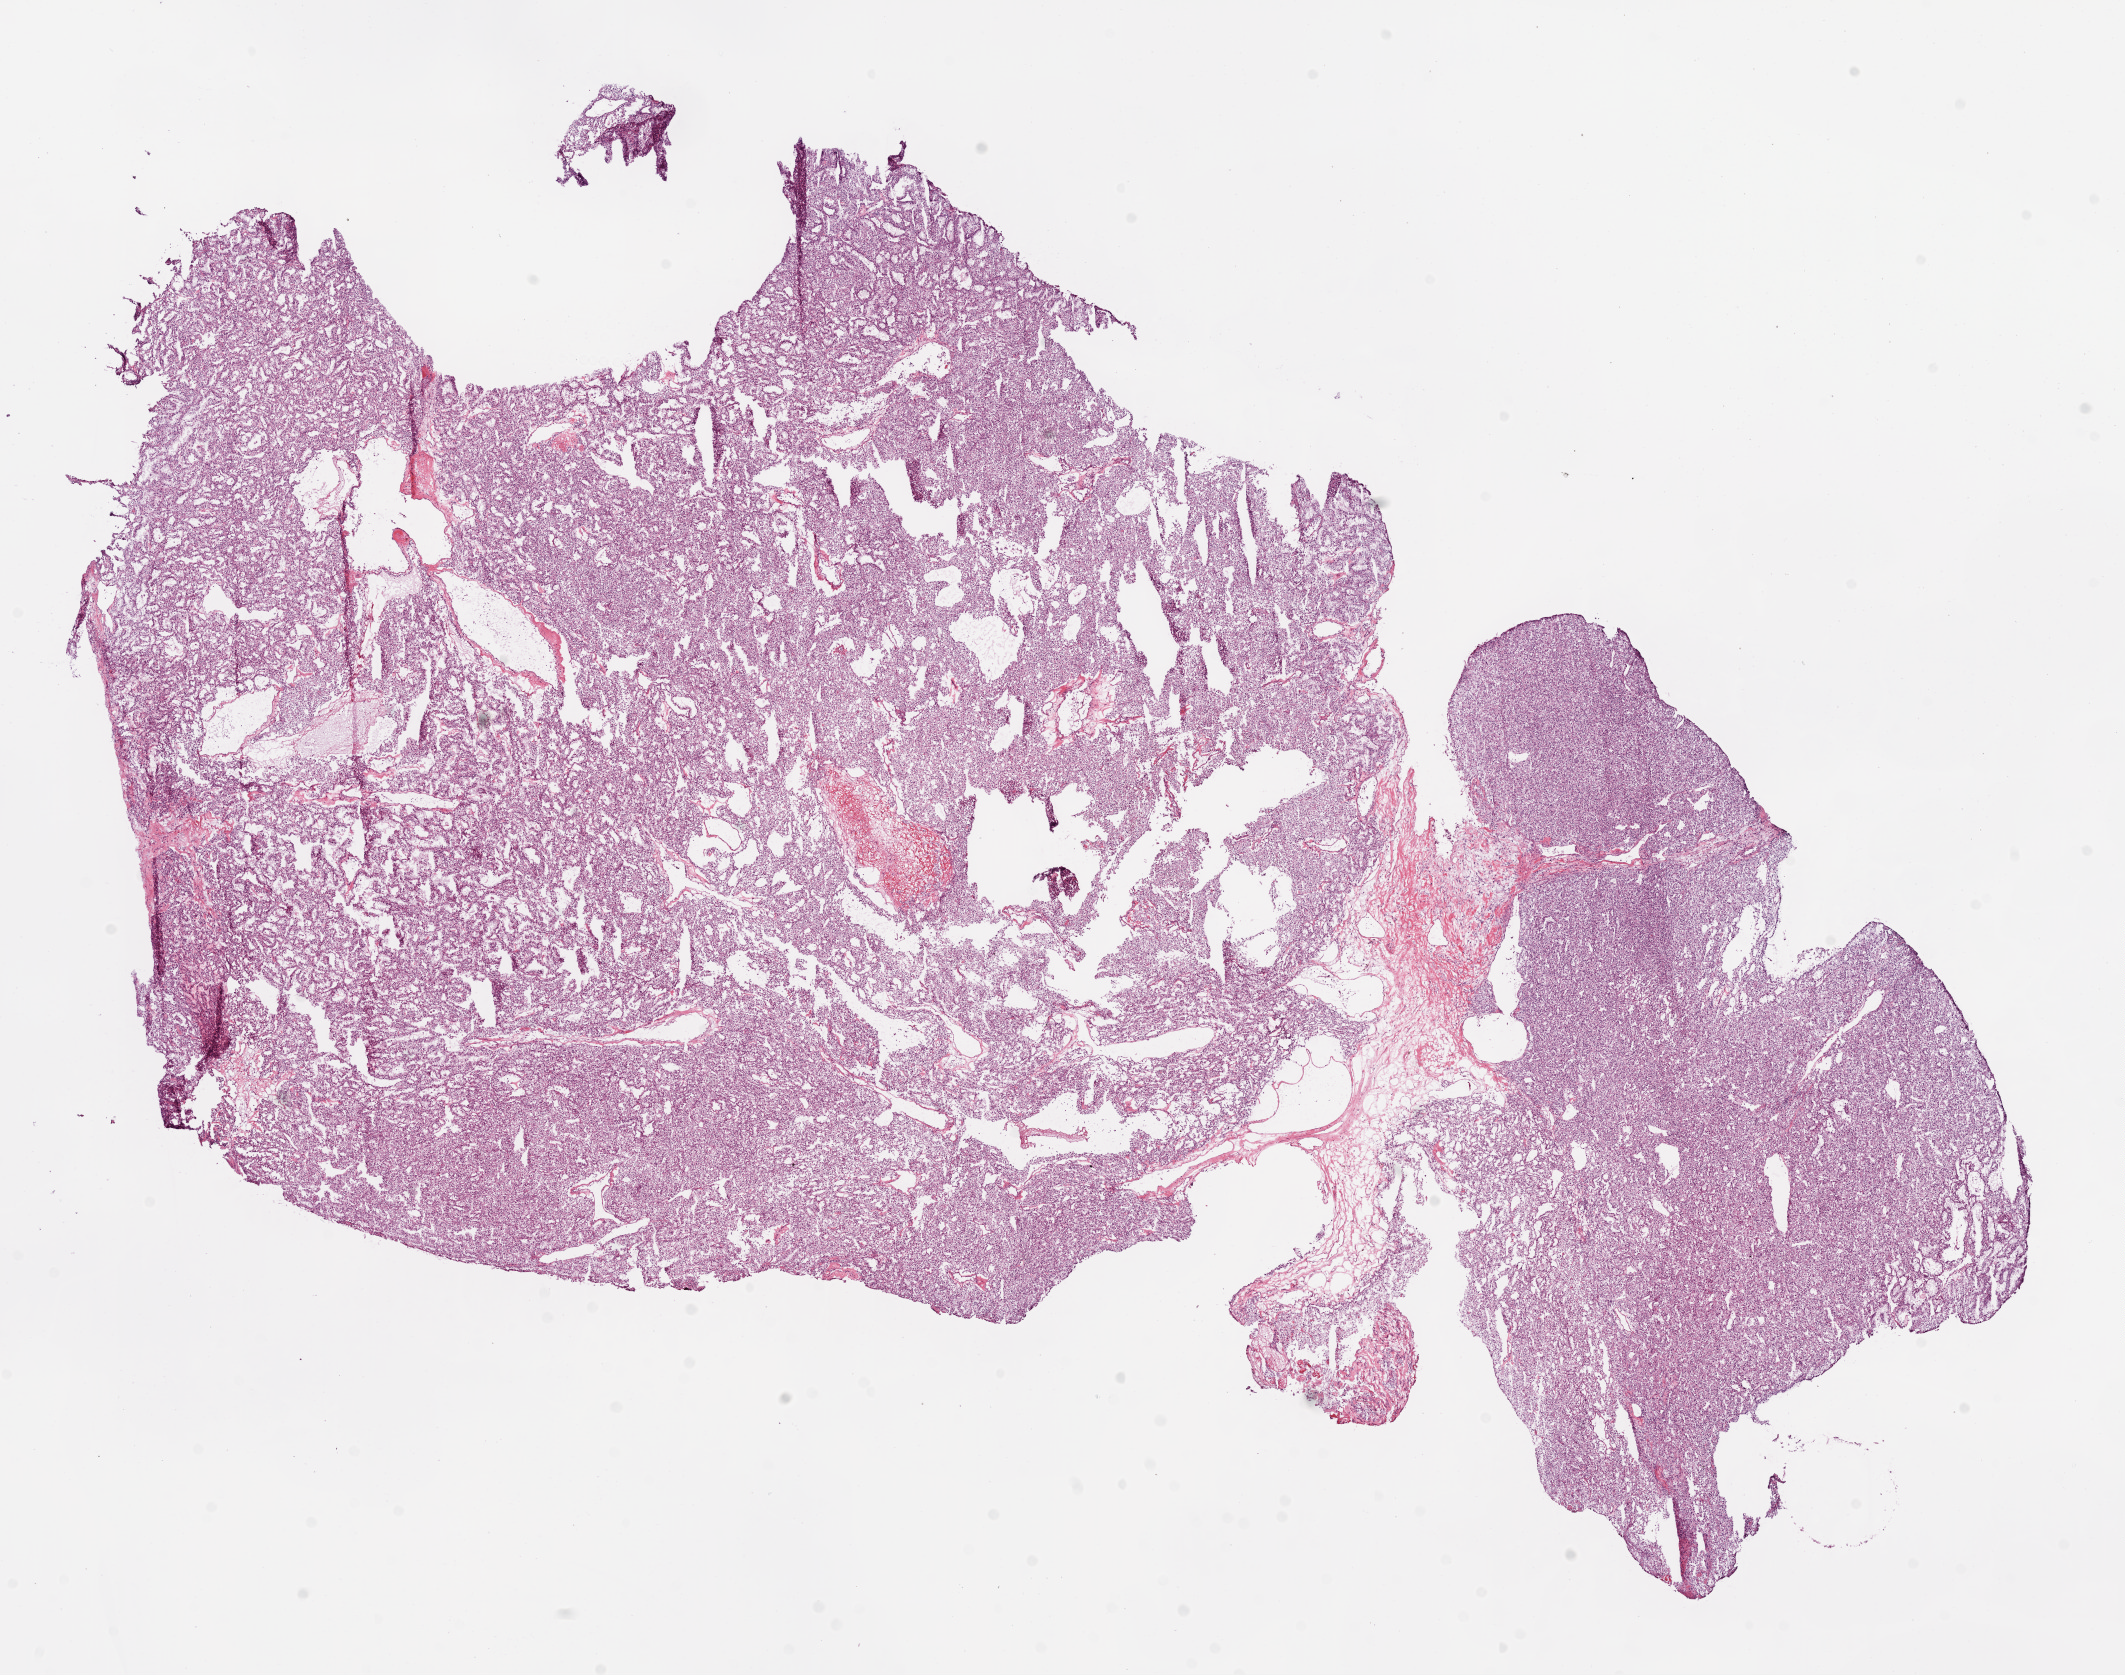
Digitized H&E-stained tissue section (whole slide) — low-resolution overview of the scanned area, about 17.1 x 13.4 mm (from a 20x scan), frozen section from the bottom of the tissue portion, kidney, primary tumour sample. Male, age 76 years at initial diagnosis. Histologic grade: G2 (moderately differentiated). Composition of this section per pathologist review: tumour cells 90%, tumour nuclei 85%, normal cells 0%, stromal cells 10%, necrosis 0%.
• TNM: T3a N0 M0
• AJCC pathologic stage: III
• lymph nodes positive (case pathology): 0 of 5 examined
• diagnosis: Clear cell adenocarcinoma, NOS